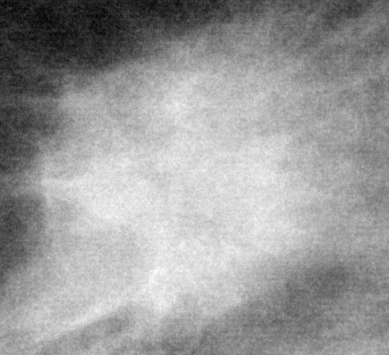
Crop from a digitized film mammogram around one marked abnormality; left breast; MLO view; BI-RADS breast density category 2 (scale 1–4).
- Mass, shape irregular, margins spiculated; BI-RADS assessment category 5; pathology (as recorded): malignant.